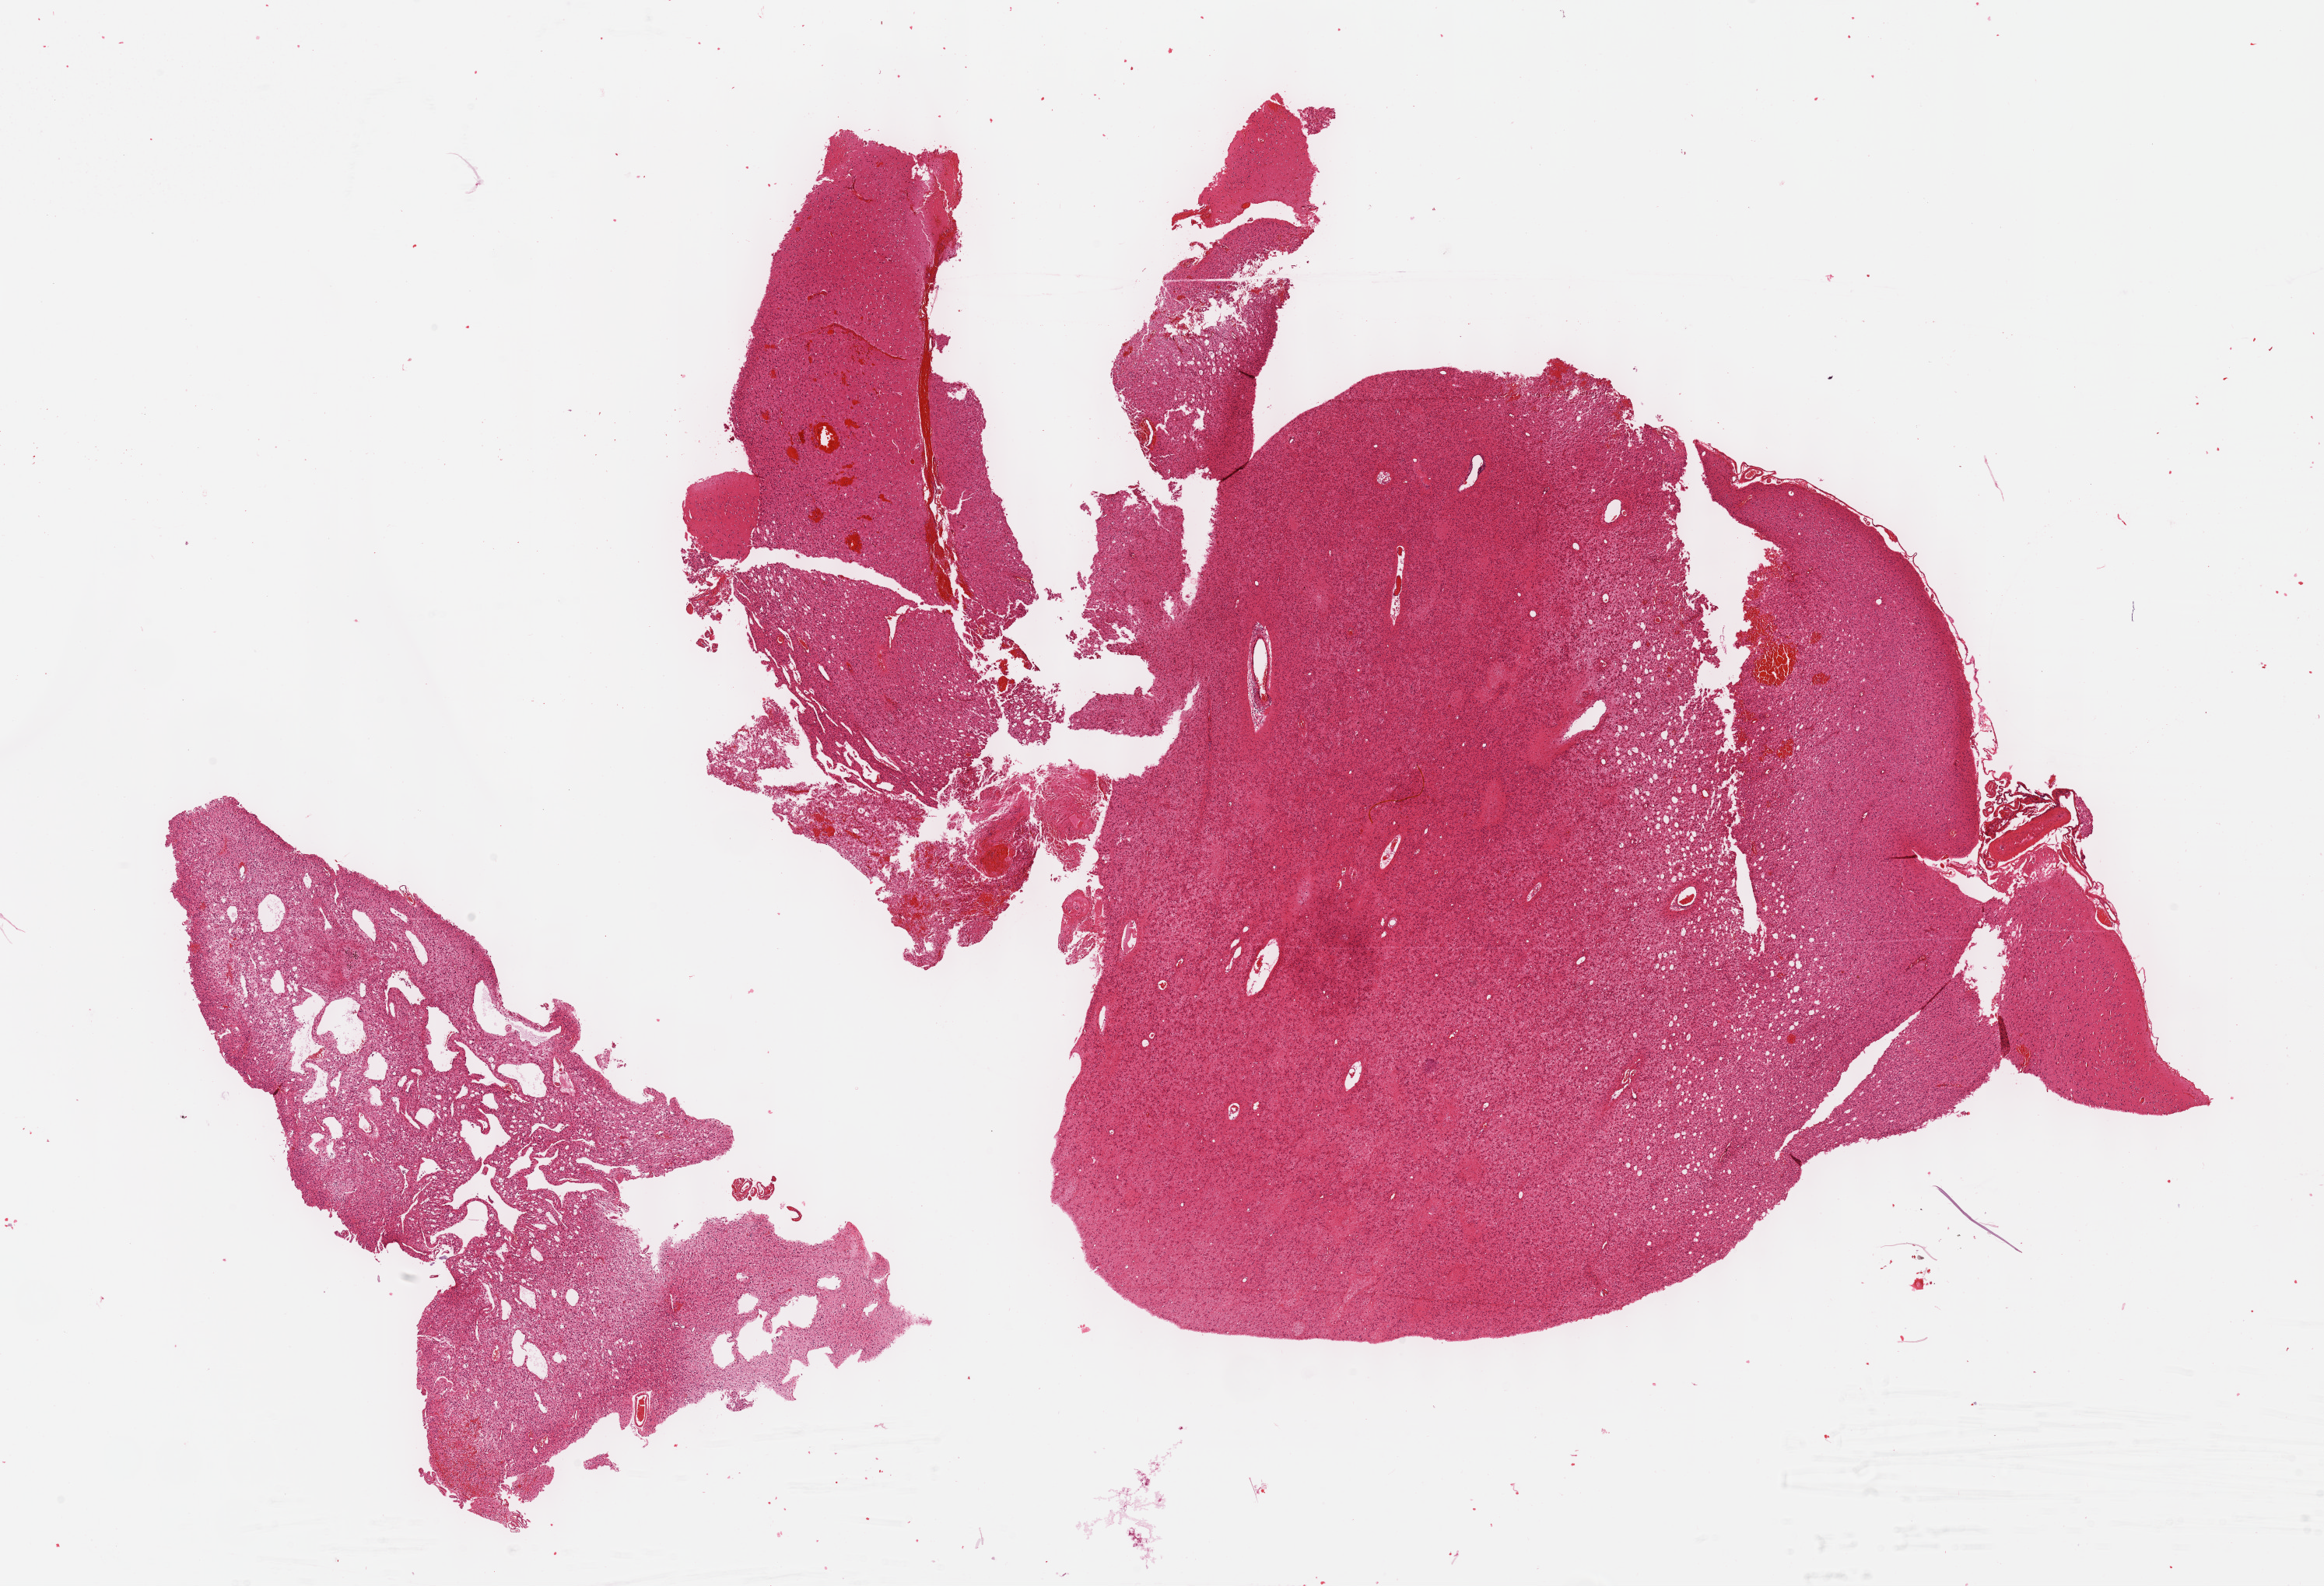
Whole-slide histology image, H&E, a low-resolution overview of the entire scanned area, about 24.2 x 16.5 mm (from a 40x scan); formalin-fixed paraffin-embedded (FFPE) diagnostic section; sample: primary tumour, brain. Male patient; age at initial diagnosis 28 years. Histologic grade: G3 (poorly differentiated).
Laterality: left. Histologic diagnosis: Astrocytoma, anaplastic.